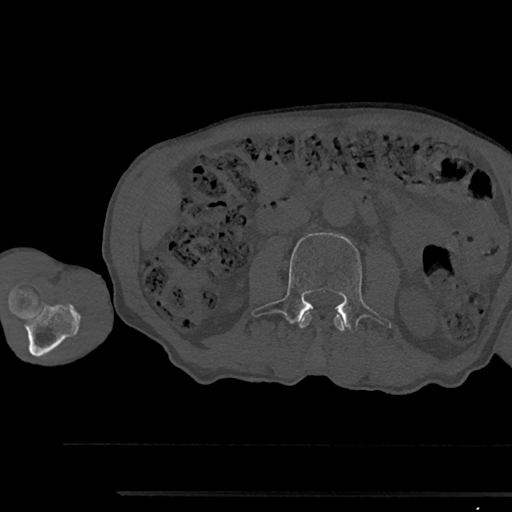
CT including the spine, one axial slice. Position 506 of 797 along the scan axis. 120 kVp. Bone window (W 1800 / L 400 HU). 512 × 512 image matrix, field of view 367 × 367 mm. Male patient, age 79 years. From the clinical record (not read from this slice): primary cancer: prostate.
Annotated regions visible in this slice (semi-automatically segmented with operator editing):
- L2 vertebra: bounding box [x1, y1, x2, y2] px = [298, 314, 345, 331]
- L3 vertebra: [252, 233, 392, 329]